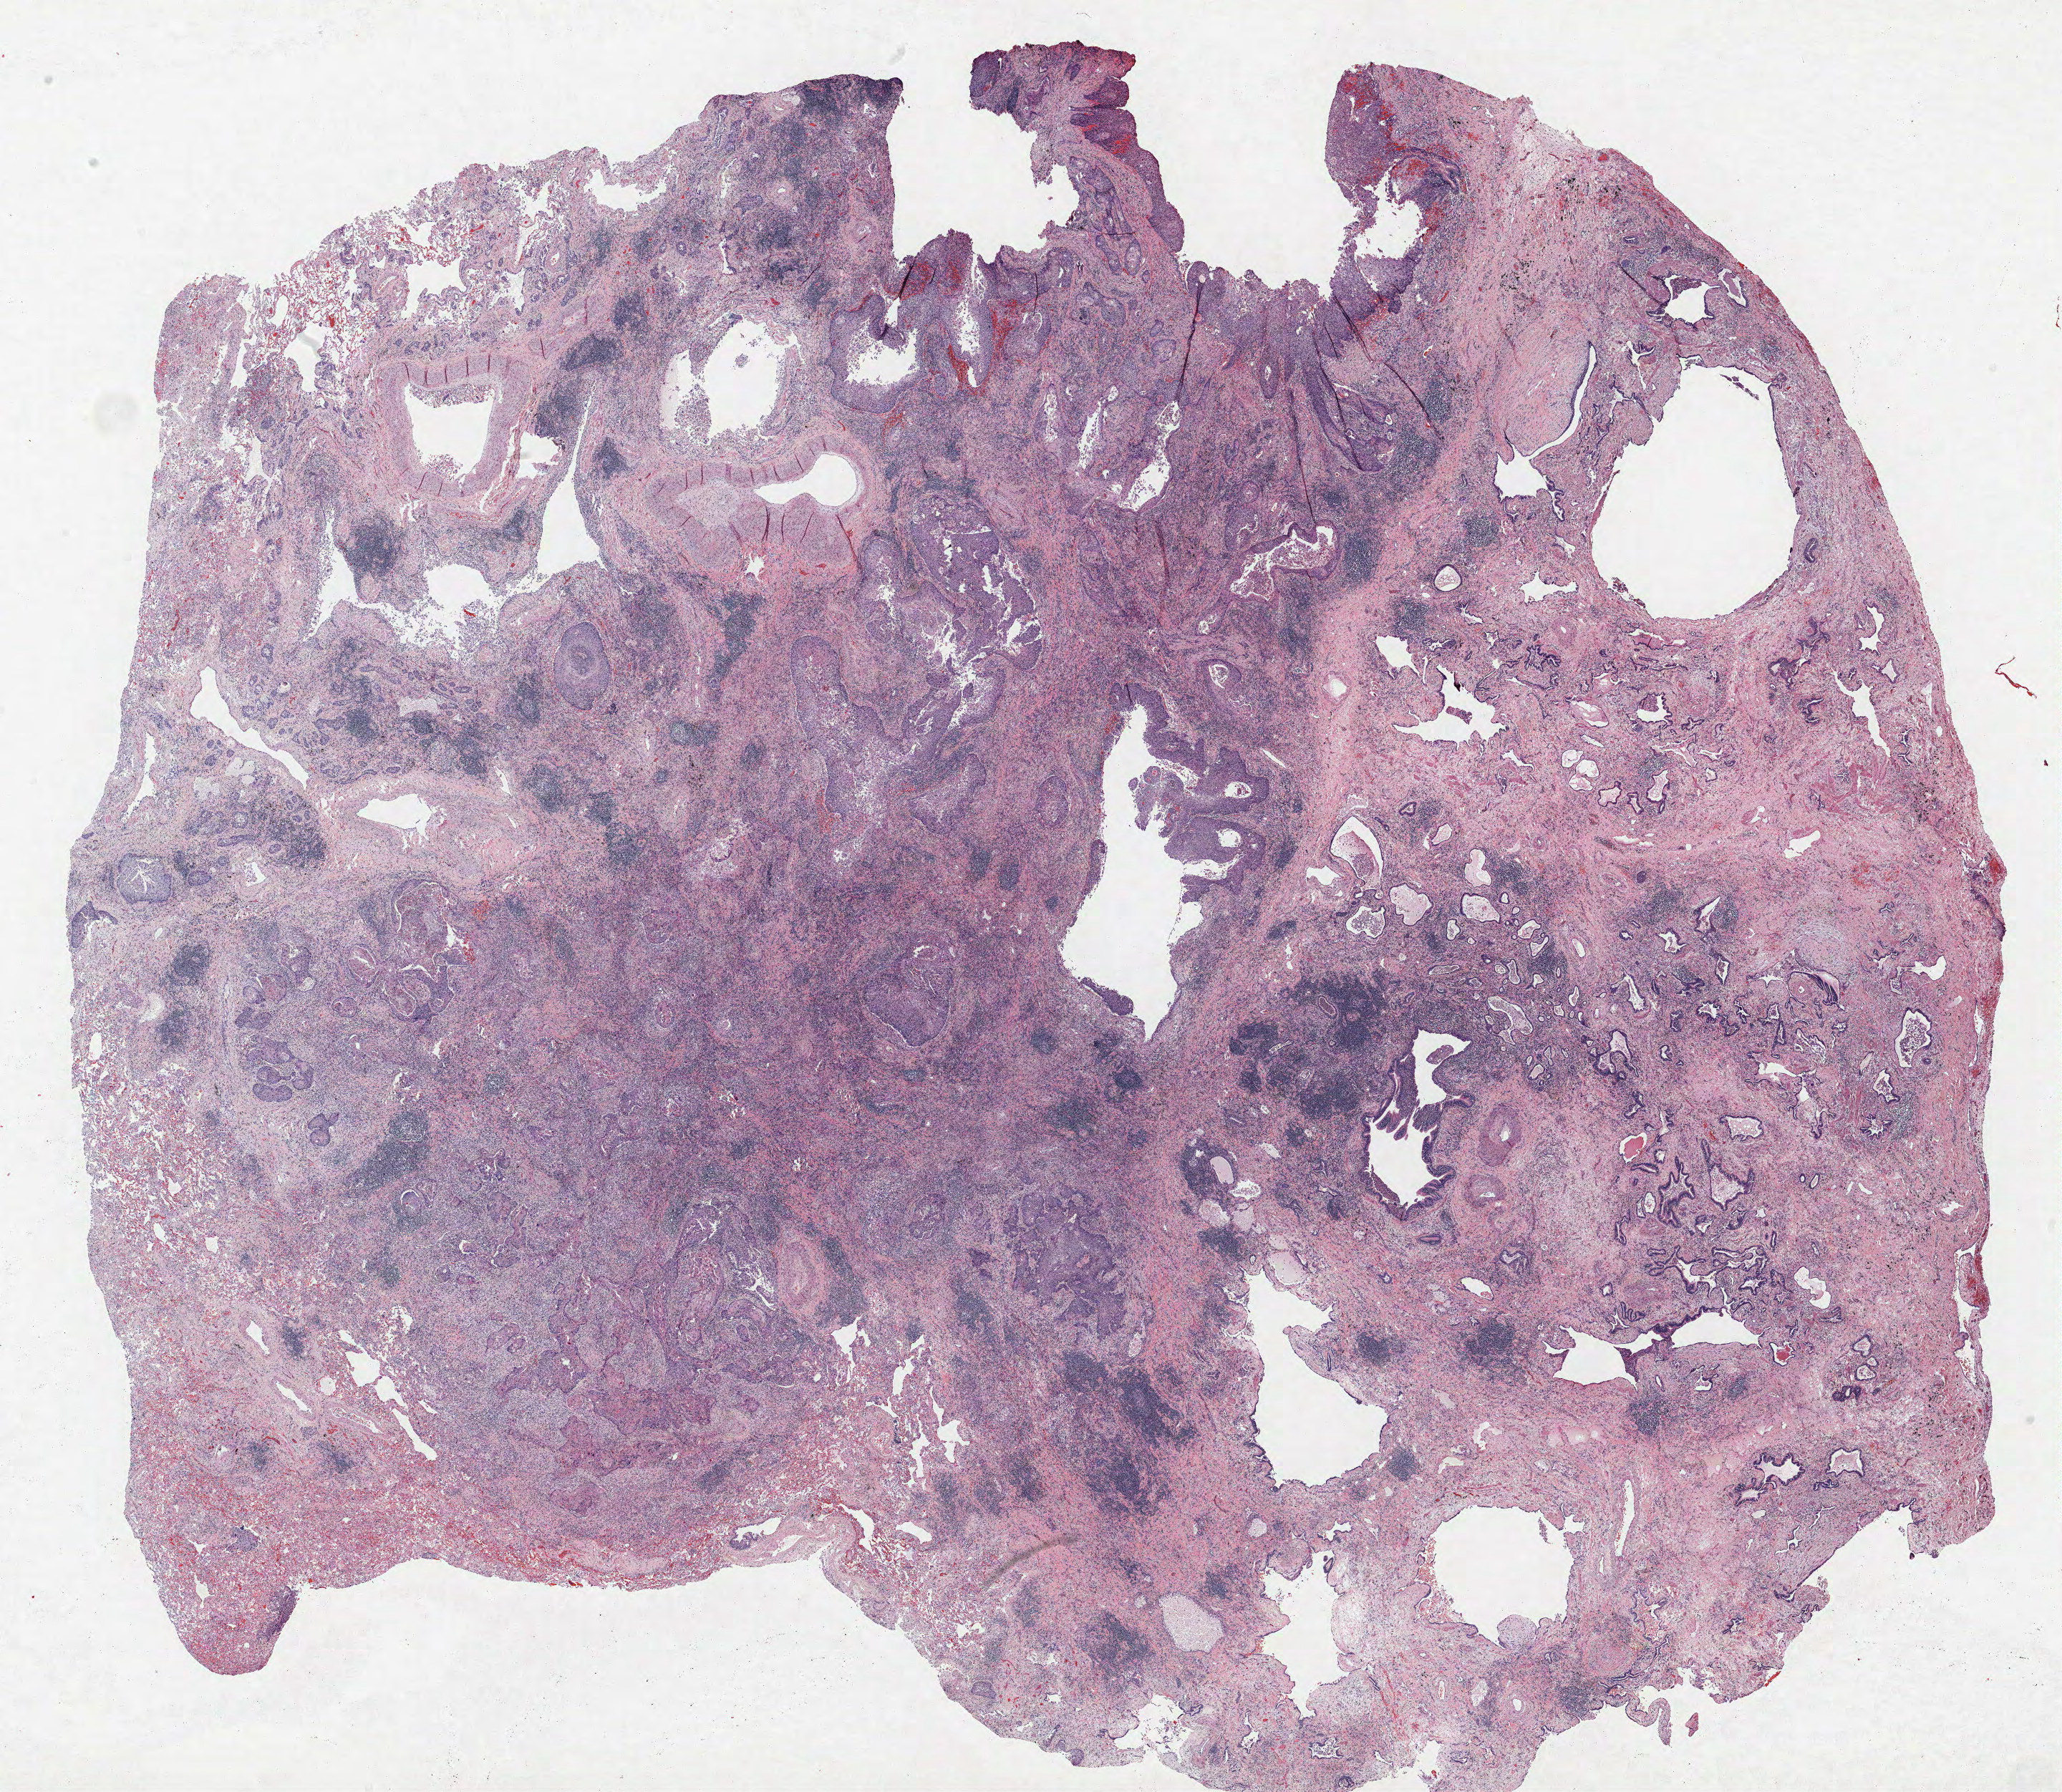
Whole-slide histology image, H&E — low-resolution overview of the scanned area, about 23.0 x 20.0 mm, FFPE section, lung. Male, age 68 at enrolment. Former smoker at enrolment. Grade: well differentiated (G1).
* participant's lung-cancer diagnosis: Squamous cell carcinoma, NOS
* primary tumour location (clinical record): left upper lobe
* tumour size (pathology): 17 mm
* stage (AJCC 6th edition): IA